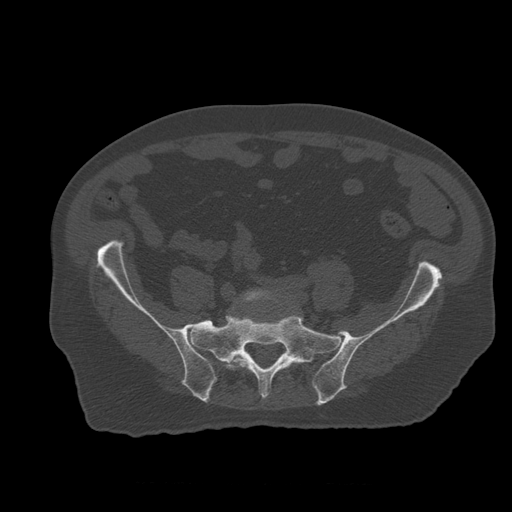
CT including the spine, one axial slice; position 125 of 399 along the scan axis; reconstruction kernel STANDARD; 120 kVp; bone window (W 1800 / L 400 HU); 512 × 512 image matrix, field of view 407 × 407 mm. Patient age 73 years. From the clinical record (not read from this slice): primary cancer: prostate; vertebrae with lytic lesions (as recorded): L2.
Structures marked on this image (semi-automatic segmentation, software-assisted and operator-edited):
- L5 vertebra: box from (x=225, y=290) to (x=276, y=371) px